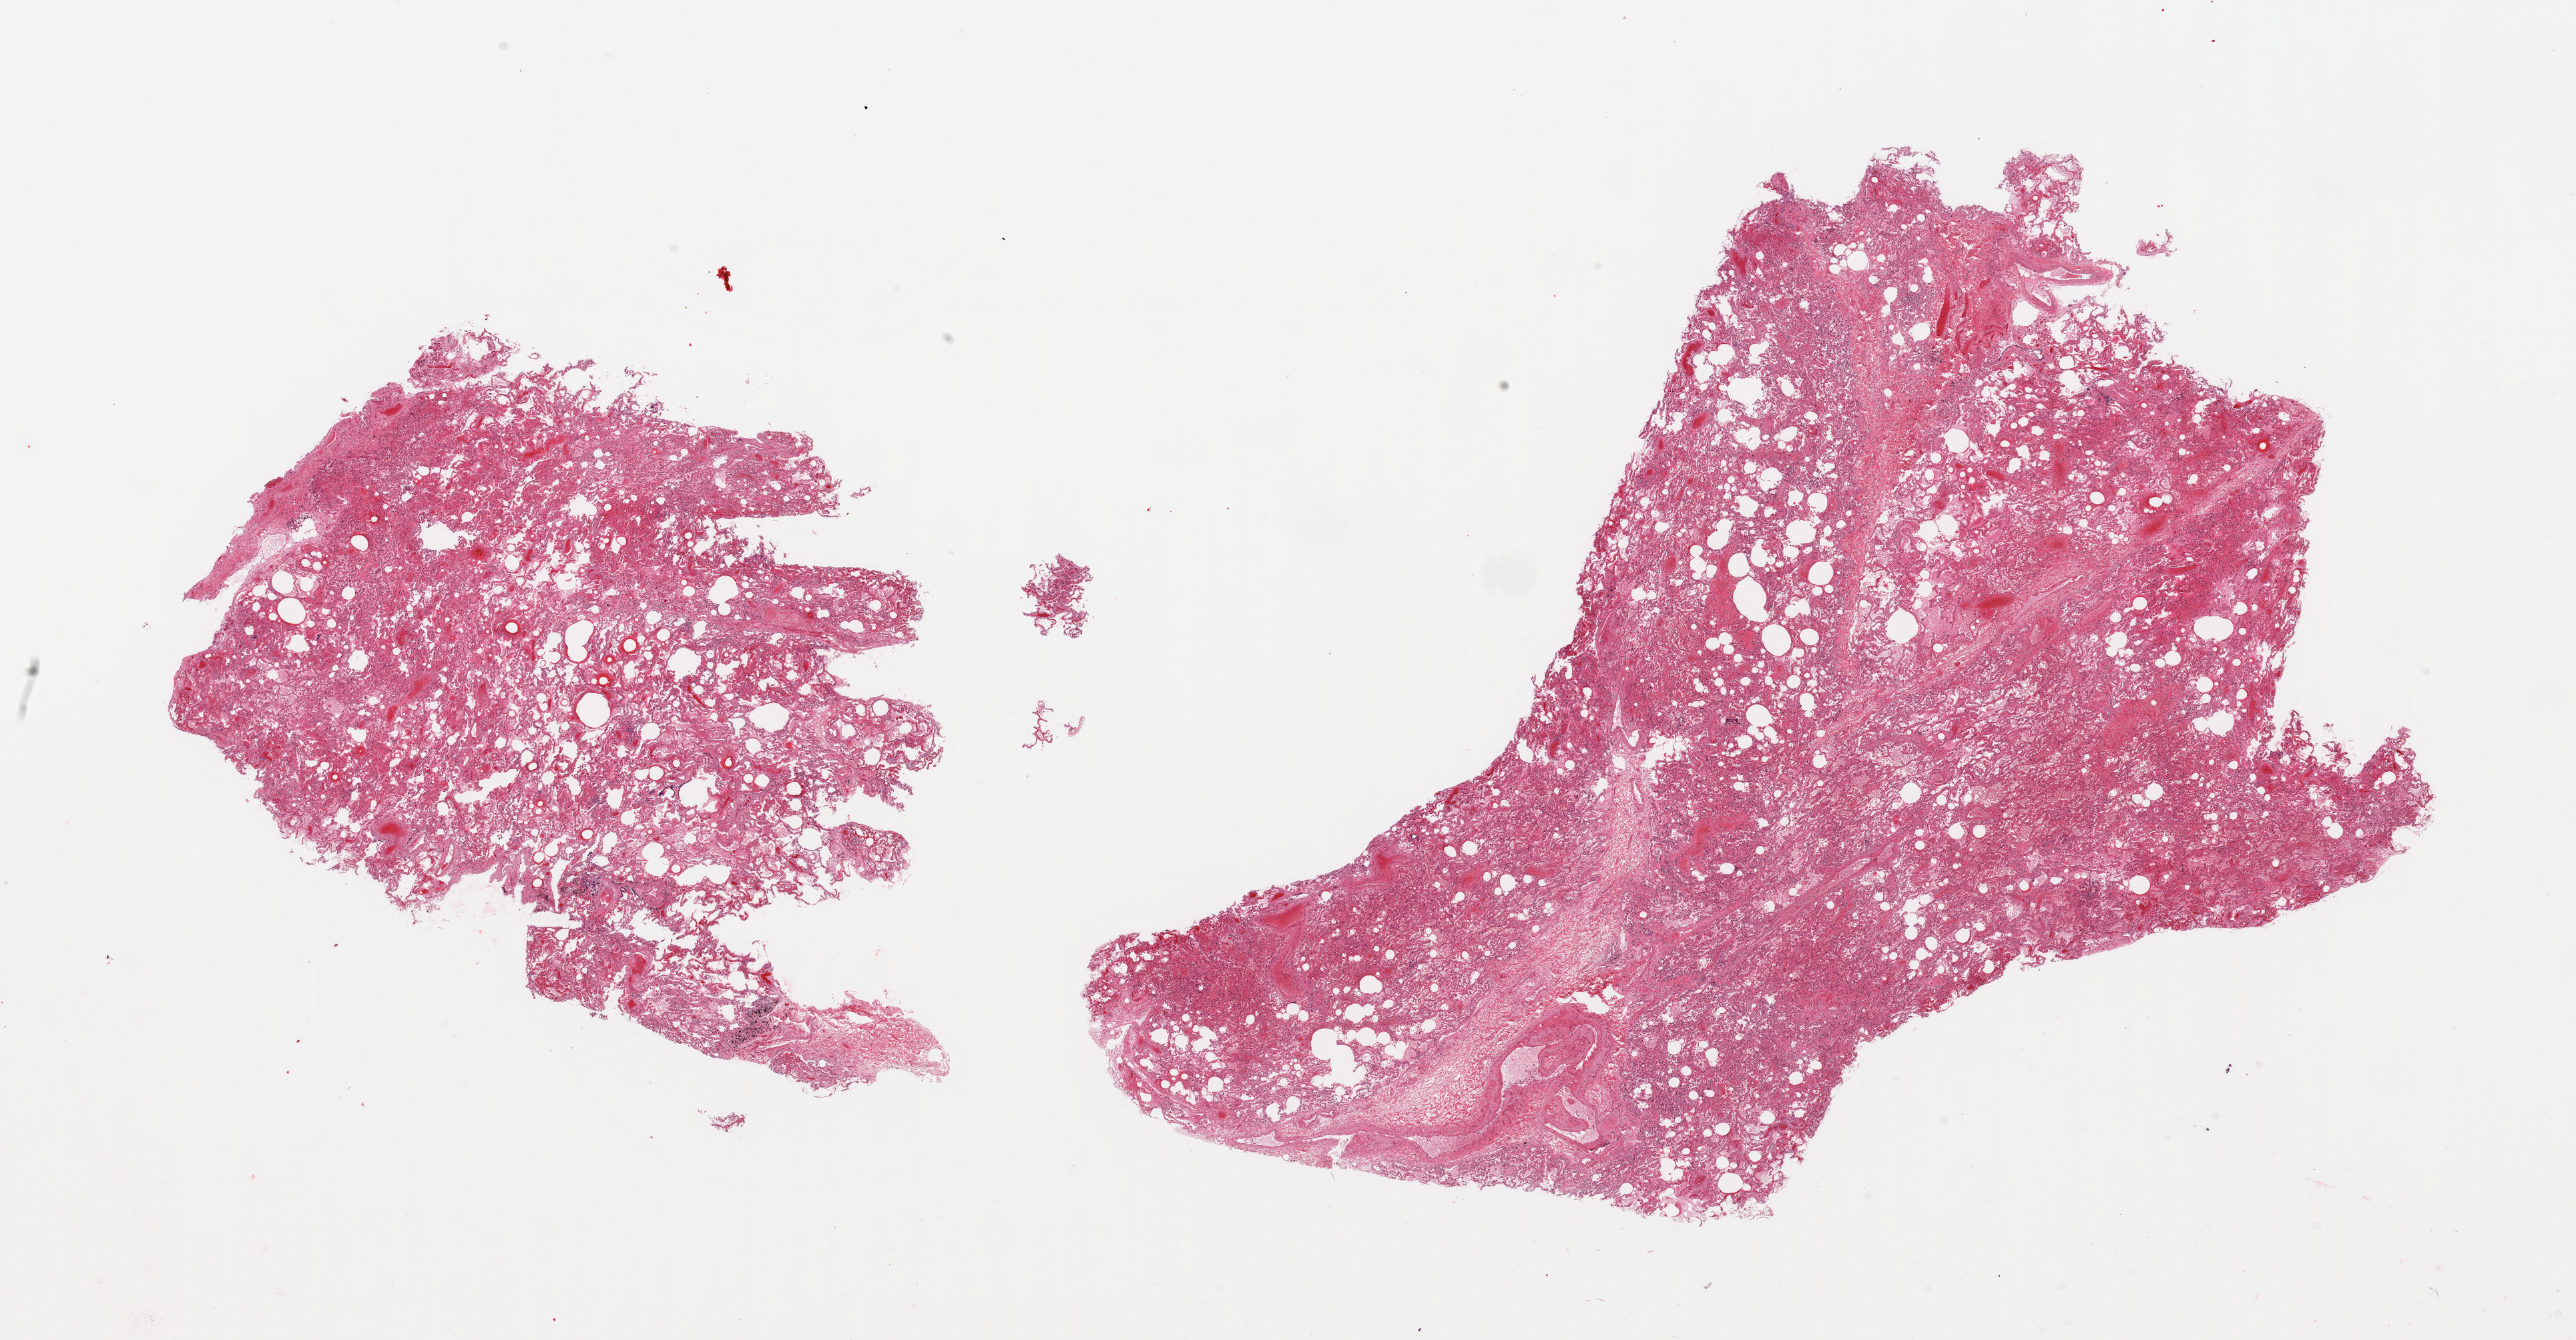
Whole-slide image, H&E stain, low-resolution overview of the scanned area, about 30.5 x 15.9 mm. PAXgene-fixed, paraffin-embedded tissue. Target tissue: lung. Donor tissue sample. Male donor.
Reviewer comment on this tissue sample: 2 pieces; congestion, hemorrhage, edema, numerous pulmonary macrophages.